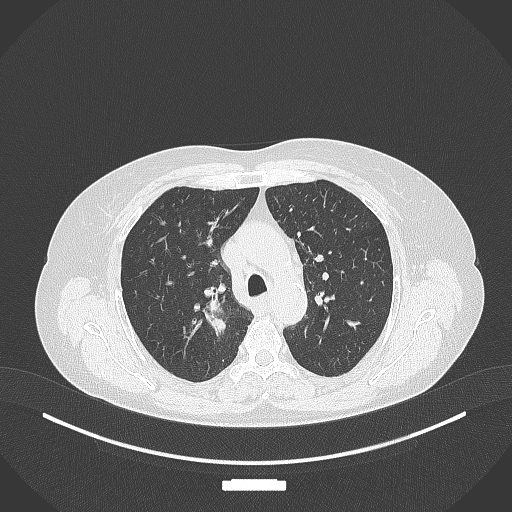
Chest CT, one axial slice. Reconstruction kernel B70f. Lung window (W 1500 / L -600 HU). 1 mm slice thickness. 512 × 512 image matrix, field of view 400 × 400 mm. Patient: female, 62 years. From the clinical record (not read from this slice): clinical TNM (as recorded): T1c N1 M0.
Annotated regions visible in this slice (bounding box drawn by a radiologist):
- lung tumour (recorded histology: squamous cell carcinoma): bounding box (x1, y1, x2, y2) in pixels: (205, 302, 230, 341)